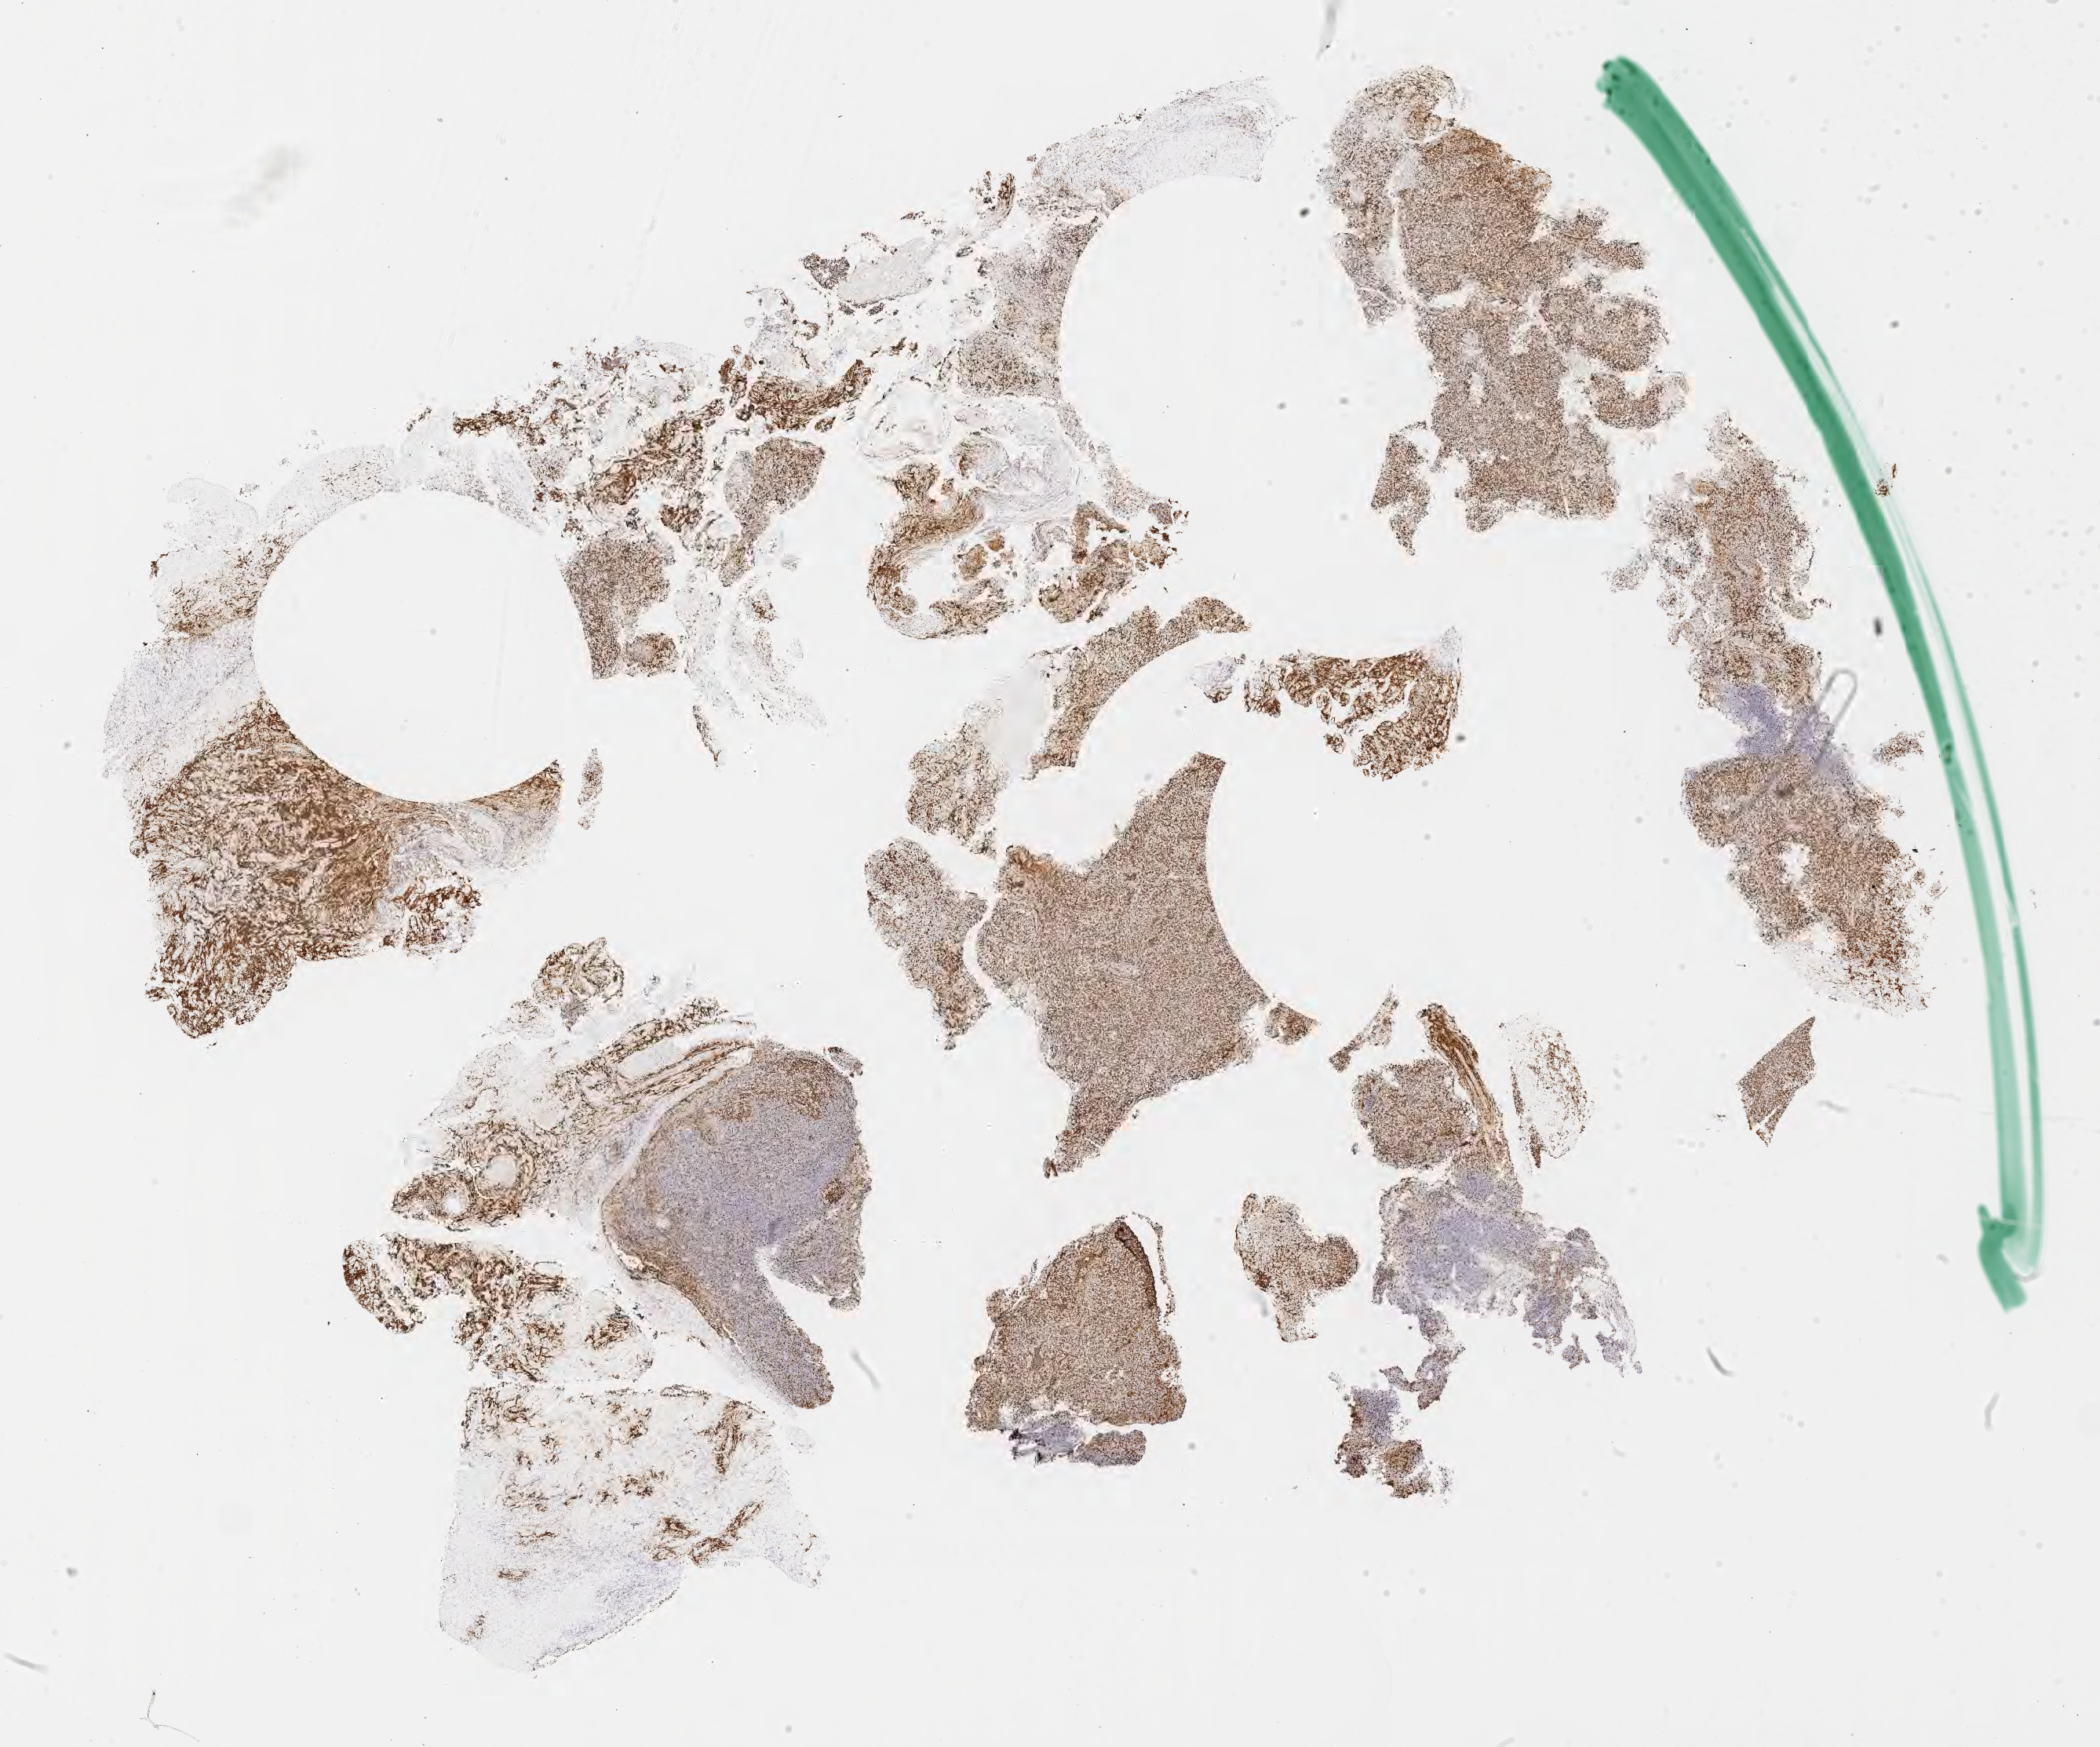
IHC for Ki-67, whole-slide image — low-resolution overview of the scanned area, about 21.6 x 18.0 mm. Specimen: tumor tissue. Anatomic site: lymph node. Patient: male, age 29 years.
• diagnosis: Diffuse large B-cell lymphoma, NOS